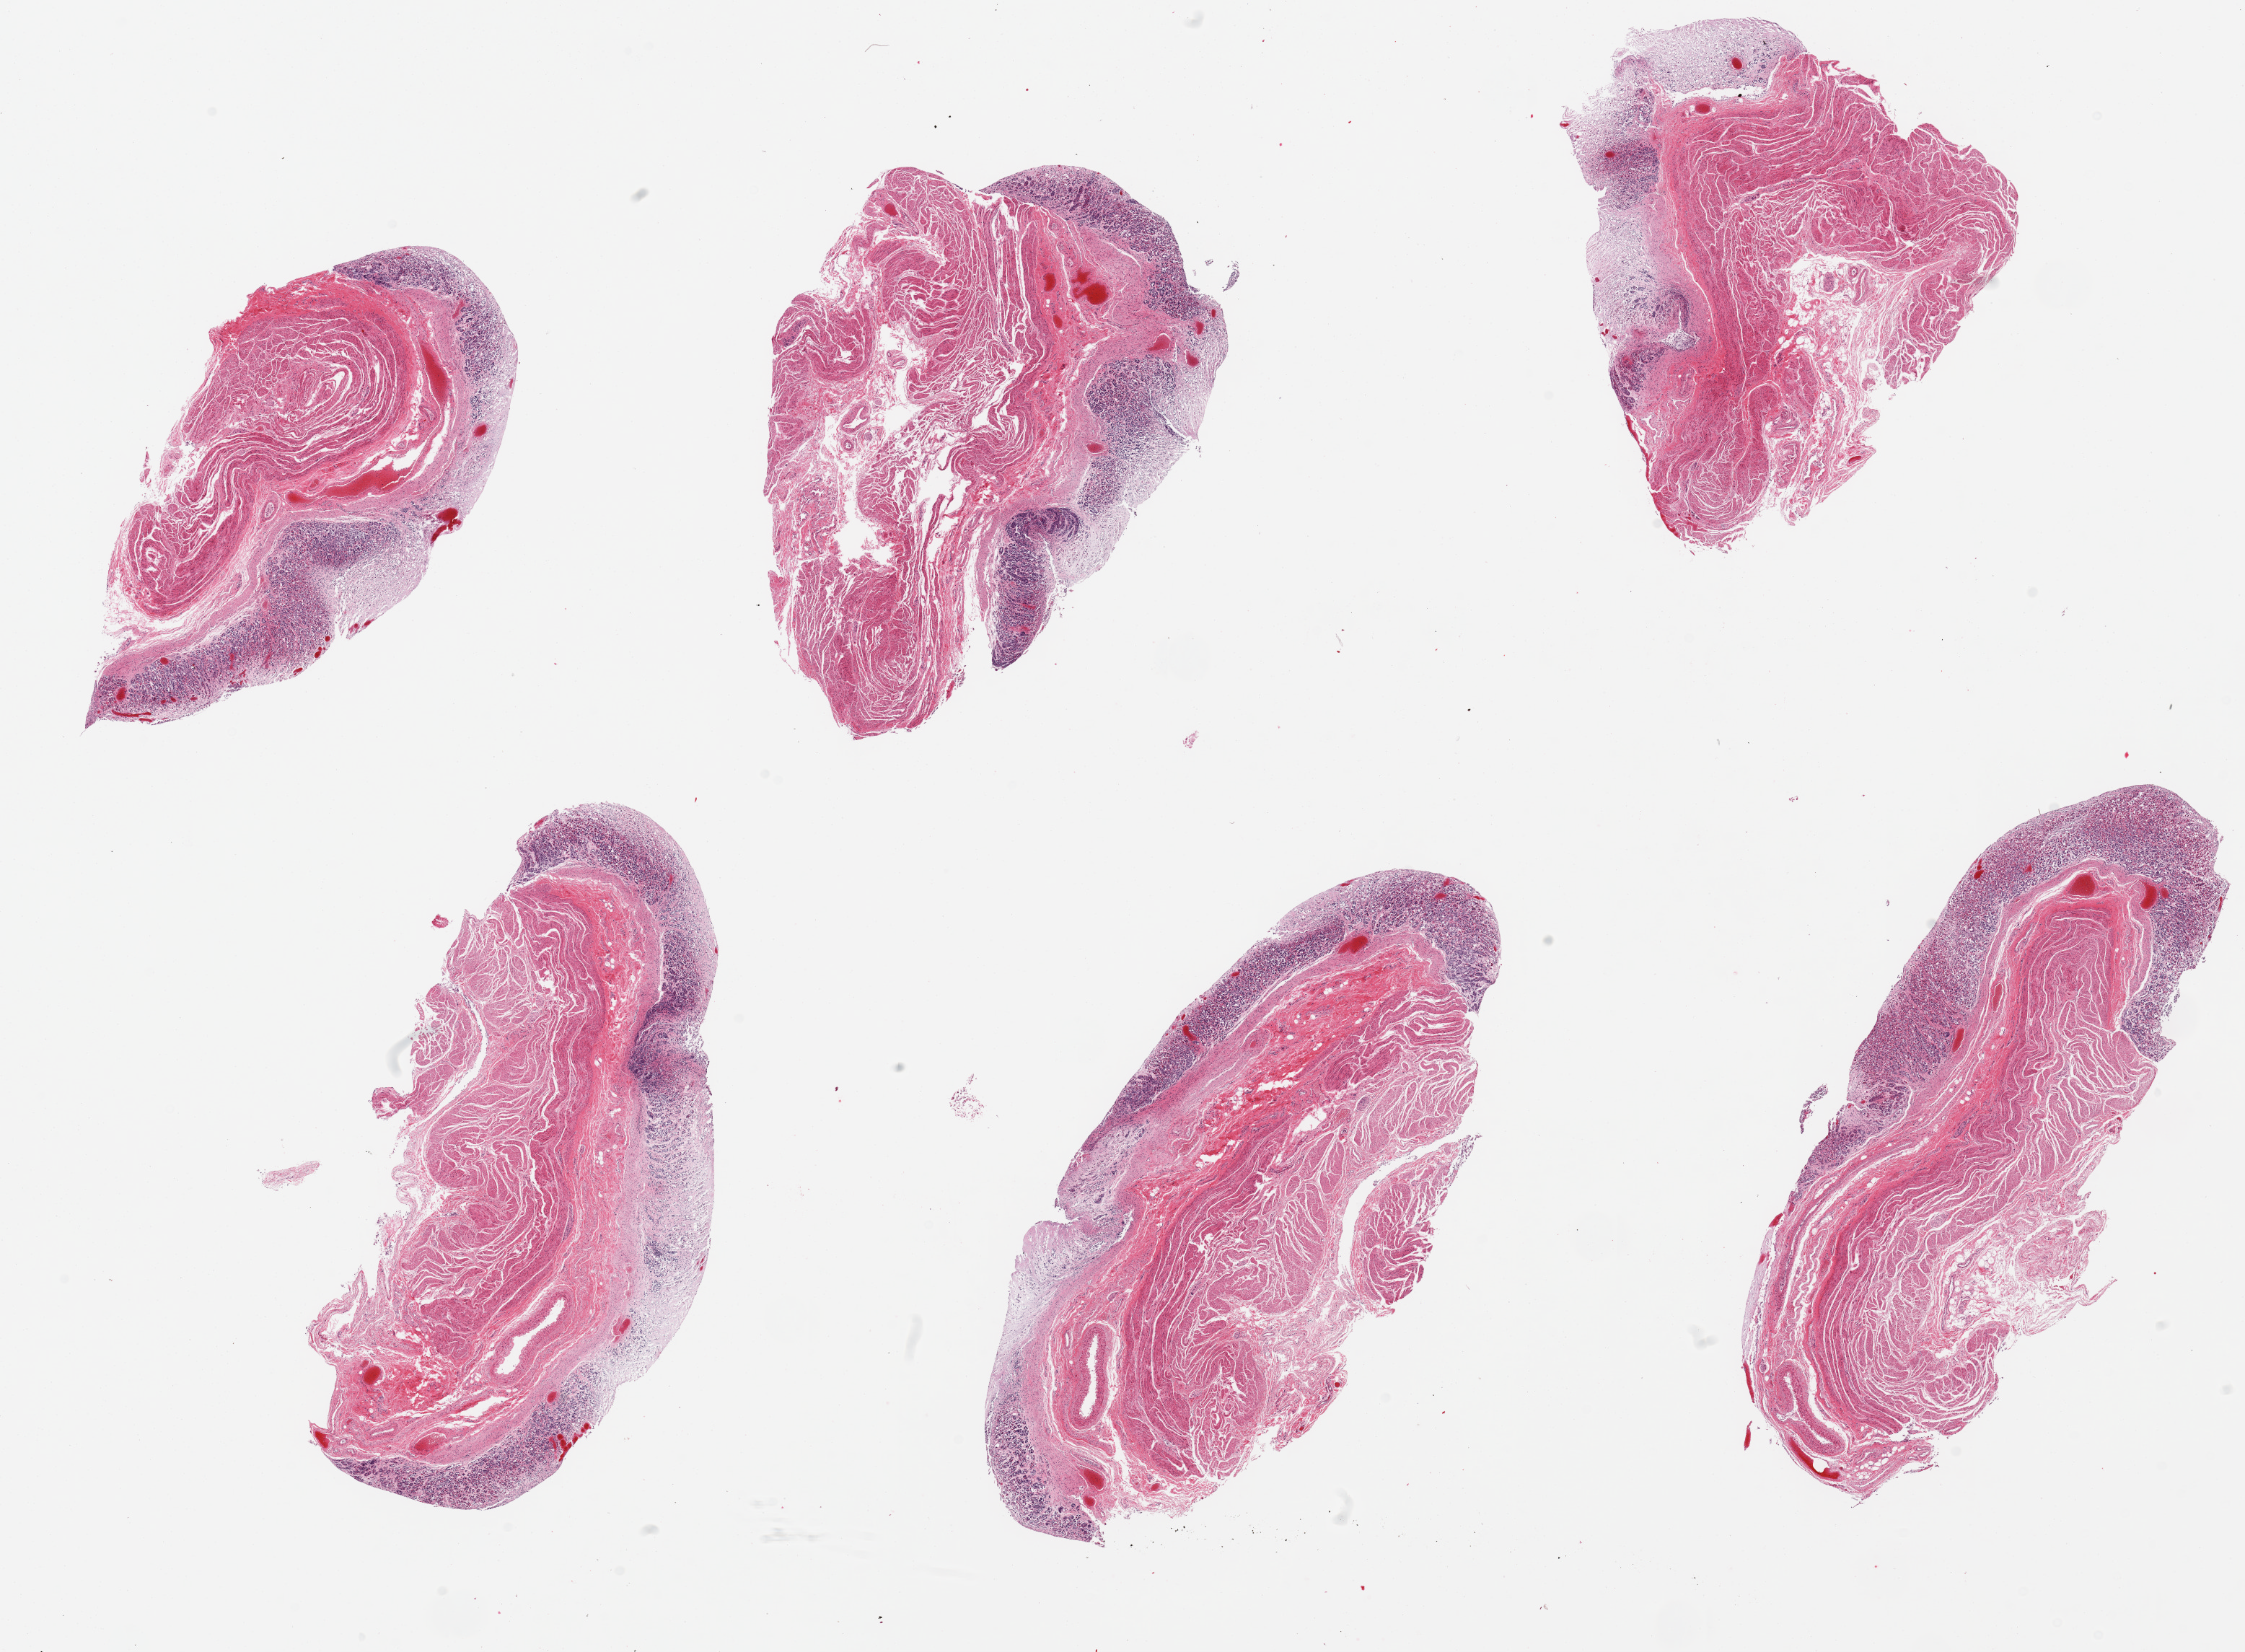
Whole-slide image, haematoxylin and eosin stain, whole scanned area (about 24.6 x 18.1 mm, acquisition: 20x scan) shown as a low-resolution overview, PAXgene-fixed, paraffin-embedded tissue, sampled site (target tissue): stomach, donor tissue sample. Donor sex: male.
* reviewer comment on this tissue sample: 6 pieces, mucosa is ~0.8mm, 30-40% thickness, advanced autolysis